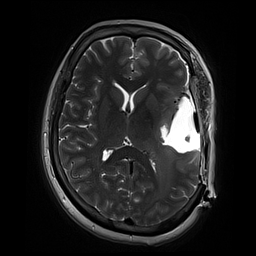
Brain MRI from a brain-tumour surgery series, one axial slice. Position 37 of 70 along the scan axis. 256 × 256 image matrix, field of view 220 × 220 mm. Case-level facts recorded for this patient, not image findings: histopathology: Glioblastoma; WHO grade: 4; IDH mutation: no; tumour location: Left Temporal.
Structures marked on this image (expert manual segmentation):
- residual tumour: box from (x=154, y=110) to (x=175, y=142) px